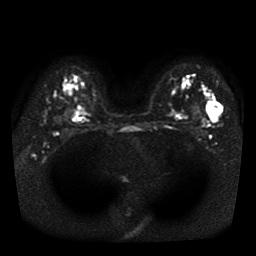
Breast MRI, one axial slice; position 30 of 41 along the scan axis; diffusion-weighted series; image 2 of 4 stored at this slice position (different b-values; order by instance number); 1.5 T; 256 × 256 image matrix, field of view 330 × 330 mm. Female patient.
Annotated regions visible in this slice (manually delineated by an expert):
- tumour on diffusion-weighted imaging: bounding box (x1, y1, x2, y2) in pixels: (209, 102, 223, 120)